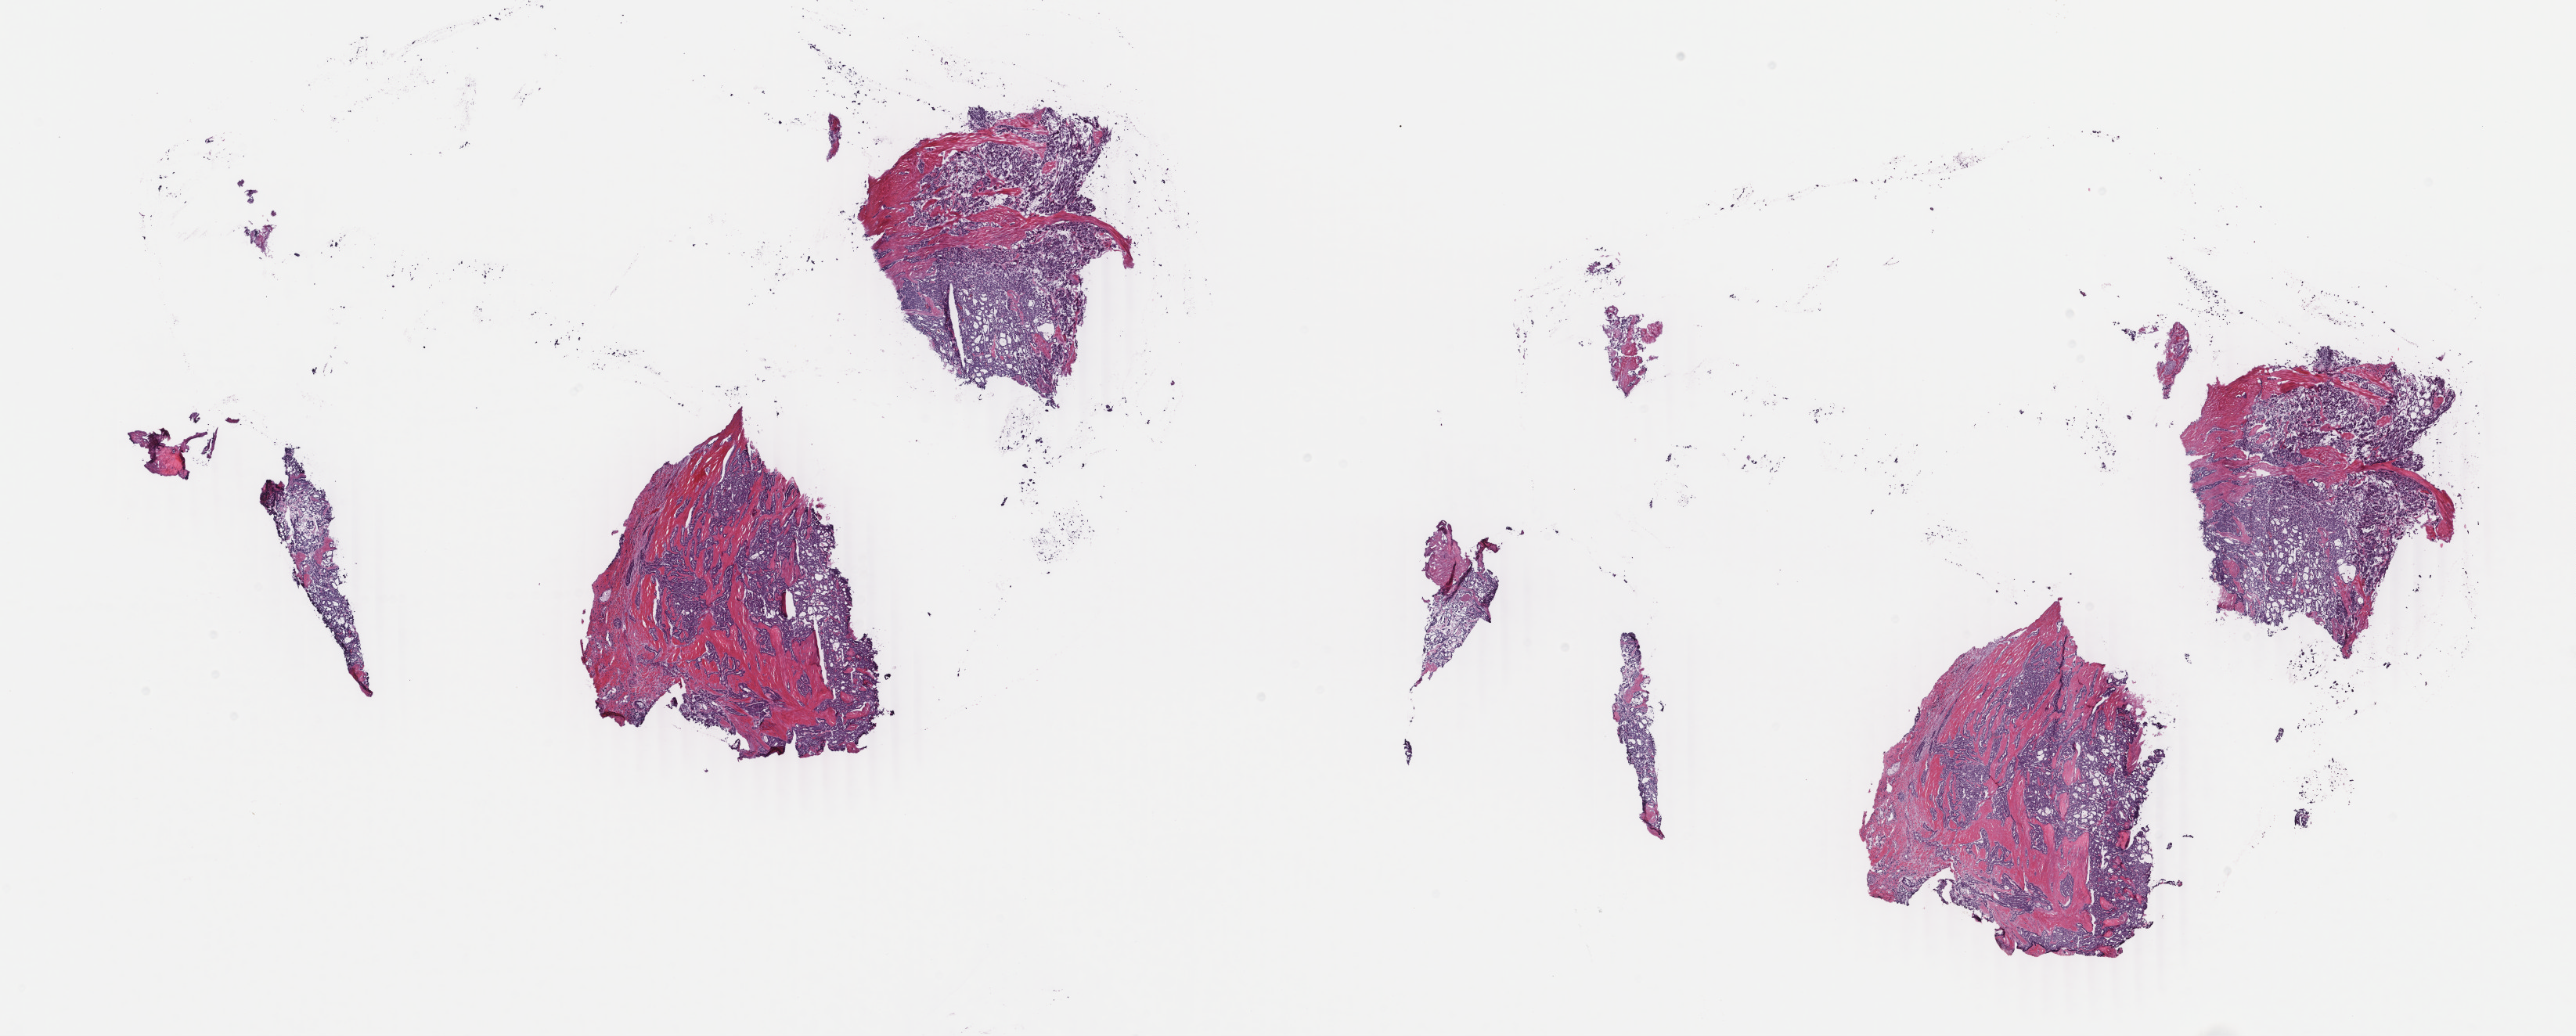
Digitized H&E tissue section (whole slide) — low-resolution overview of the scanned area, about 26.2 x 10.5 mm (from a 40x scan); frozen section; thyroid, primary tumour sample. Male patient; age at initial diagnosis 60 years. Pathologist review of this section (percent, as recorded): tumour cells 95%, tumour nuclei 95%, normal cells 0%, stromal cells 5%, necrosis 0%. Infiltration values recorded for this section: lymphocyte infiltration 0%, monocyte infiltration 0%, neutrophil infiltration 0%.
TNM: T3 N0 M0. Laterality: right. Diagnosis: Papillary adenocarcinoma, NOS (thyroid gland). AJCC pathologic stage: III (7th edition).